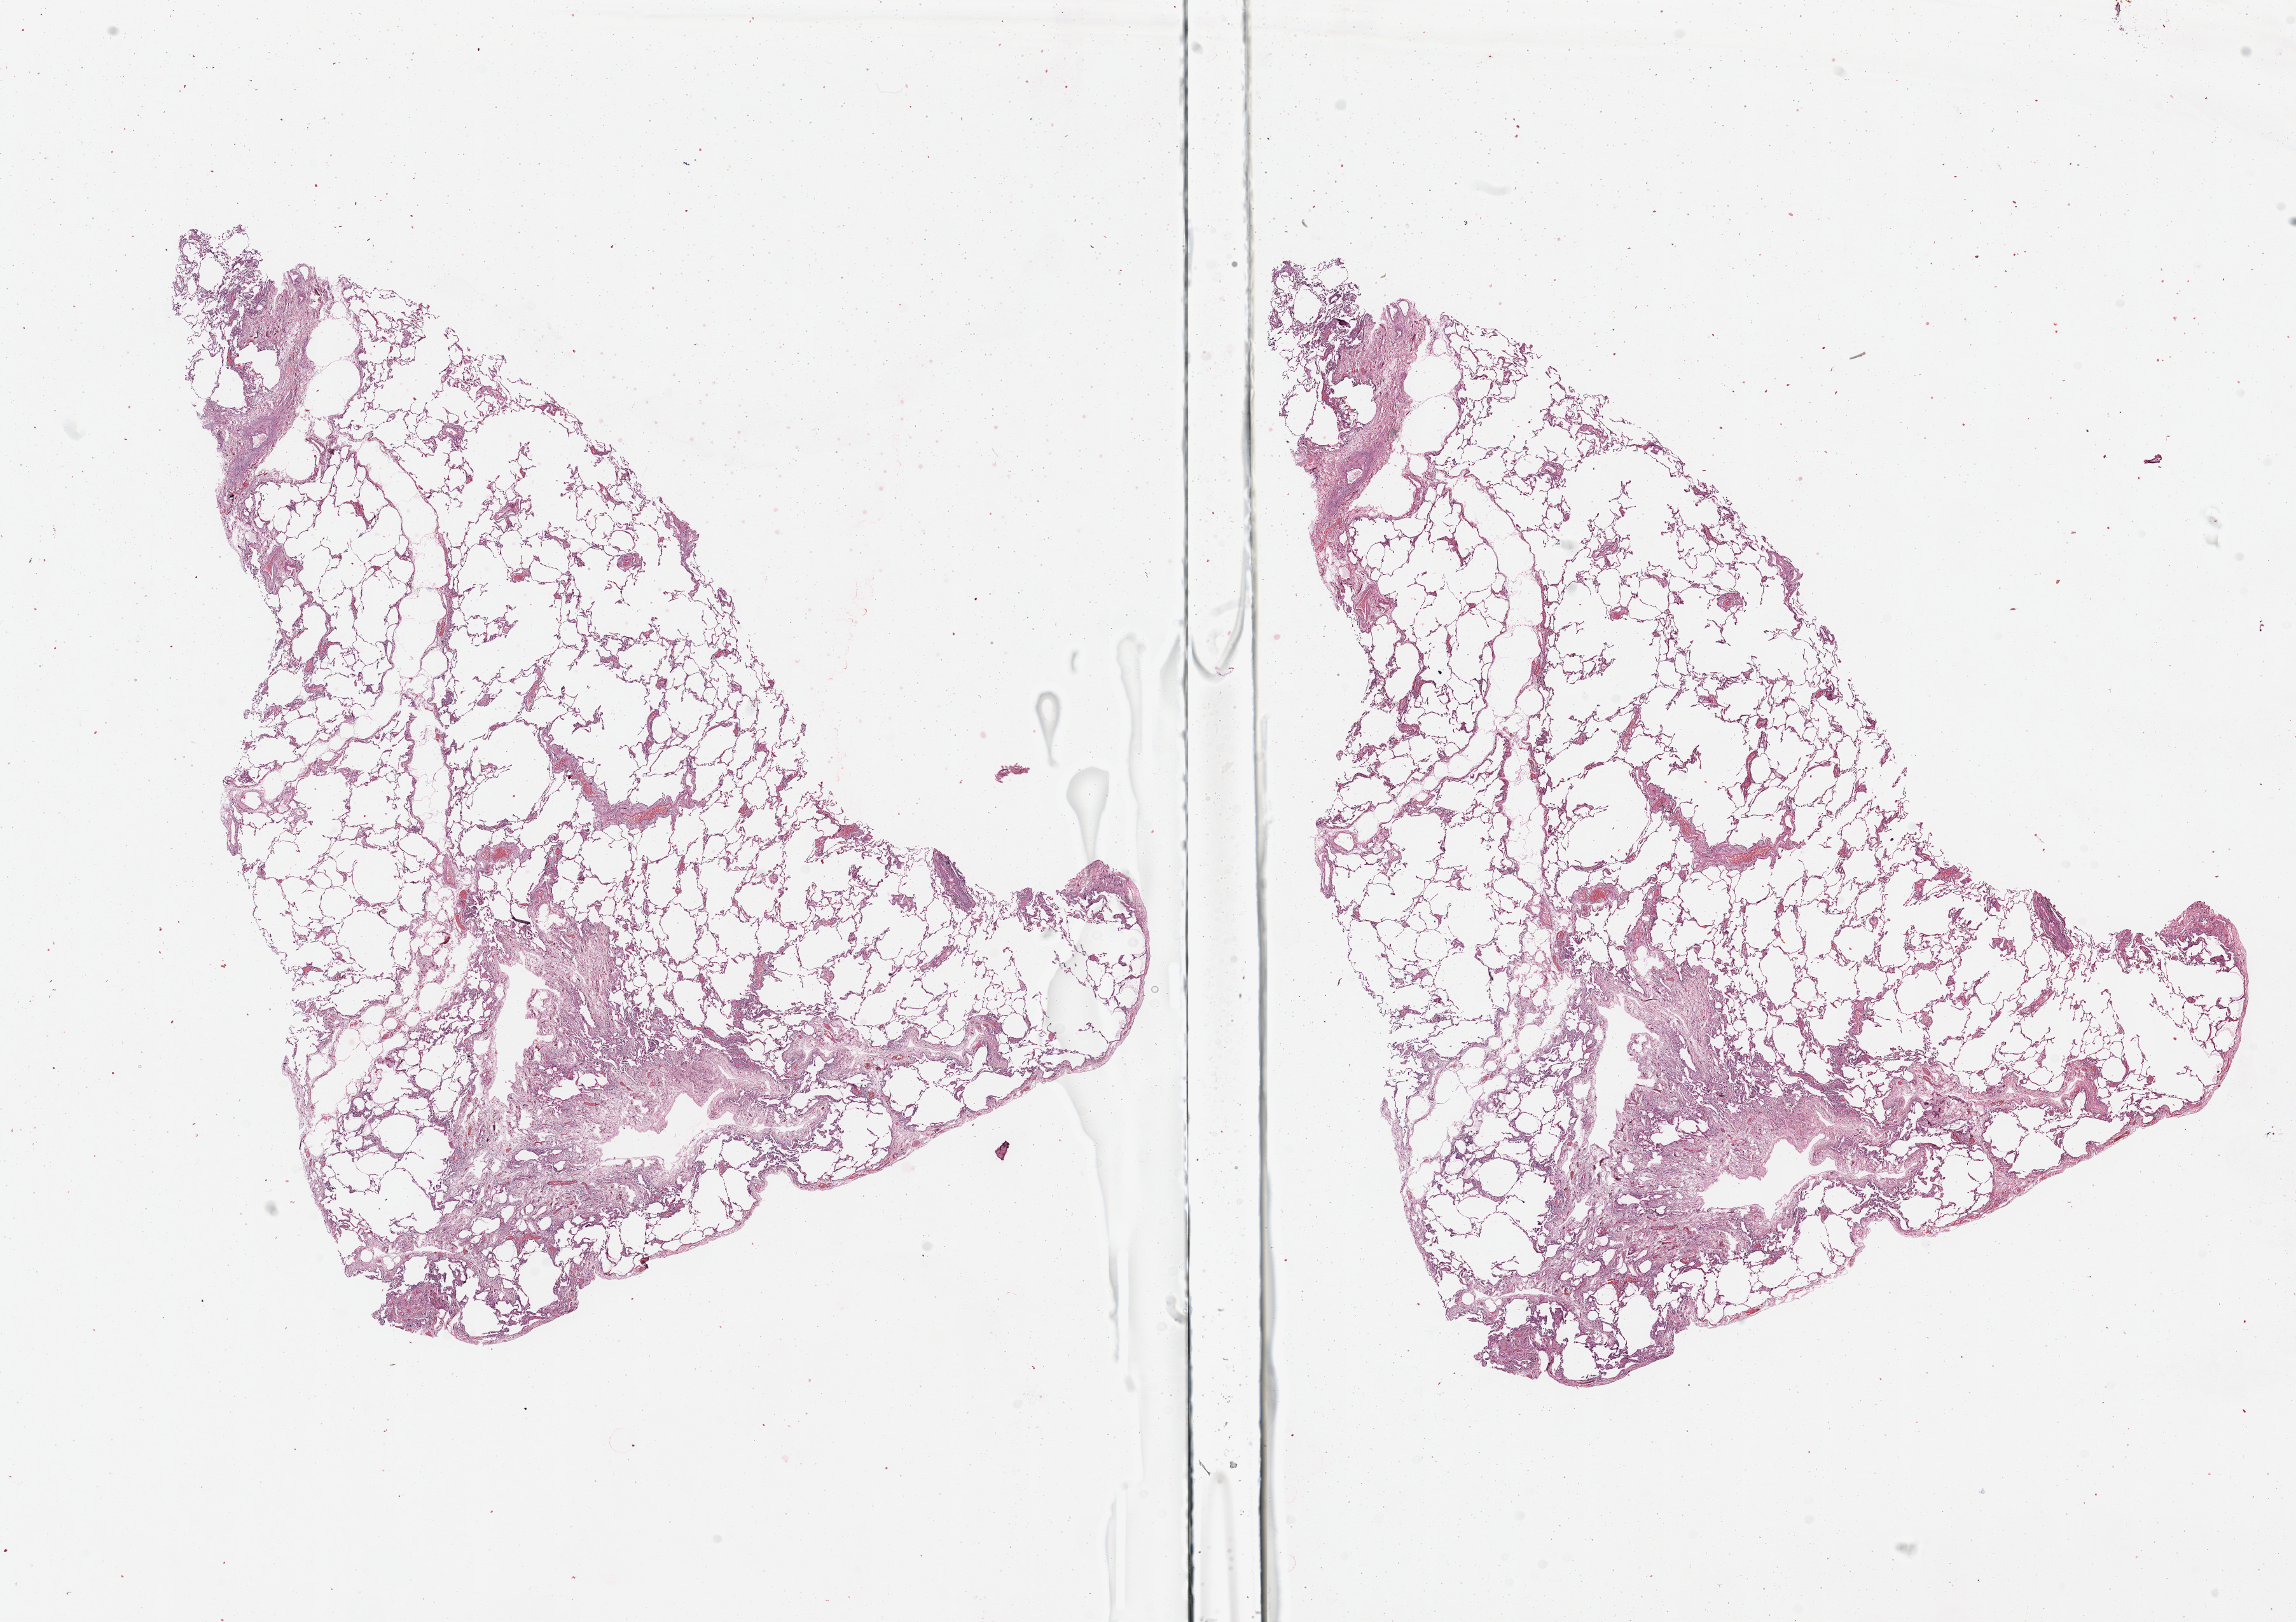
Whole-slide histology image, Hematoxylin and eosin (H&E) stained — low-resolution overview of the scanned area, about 28.5 x 20.2 mm, normal (non-tumour) tissue sample, sampled site: lung. Female, 70 y/o.
This section: normal (non-tumour) tissue from the same patient. Patient diagnosis: Adenocarcinoma, NOS.